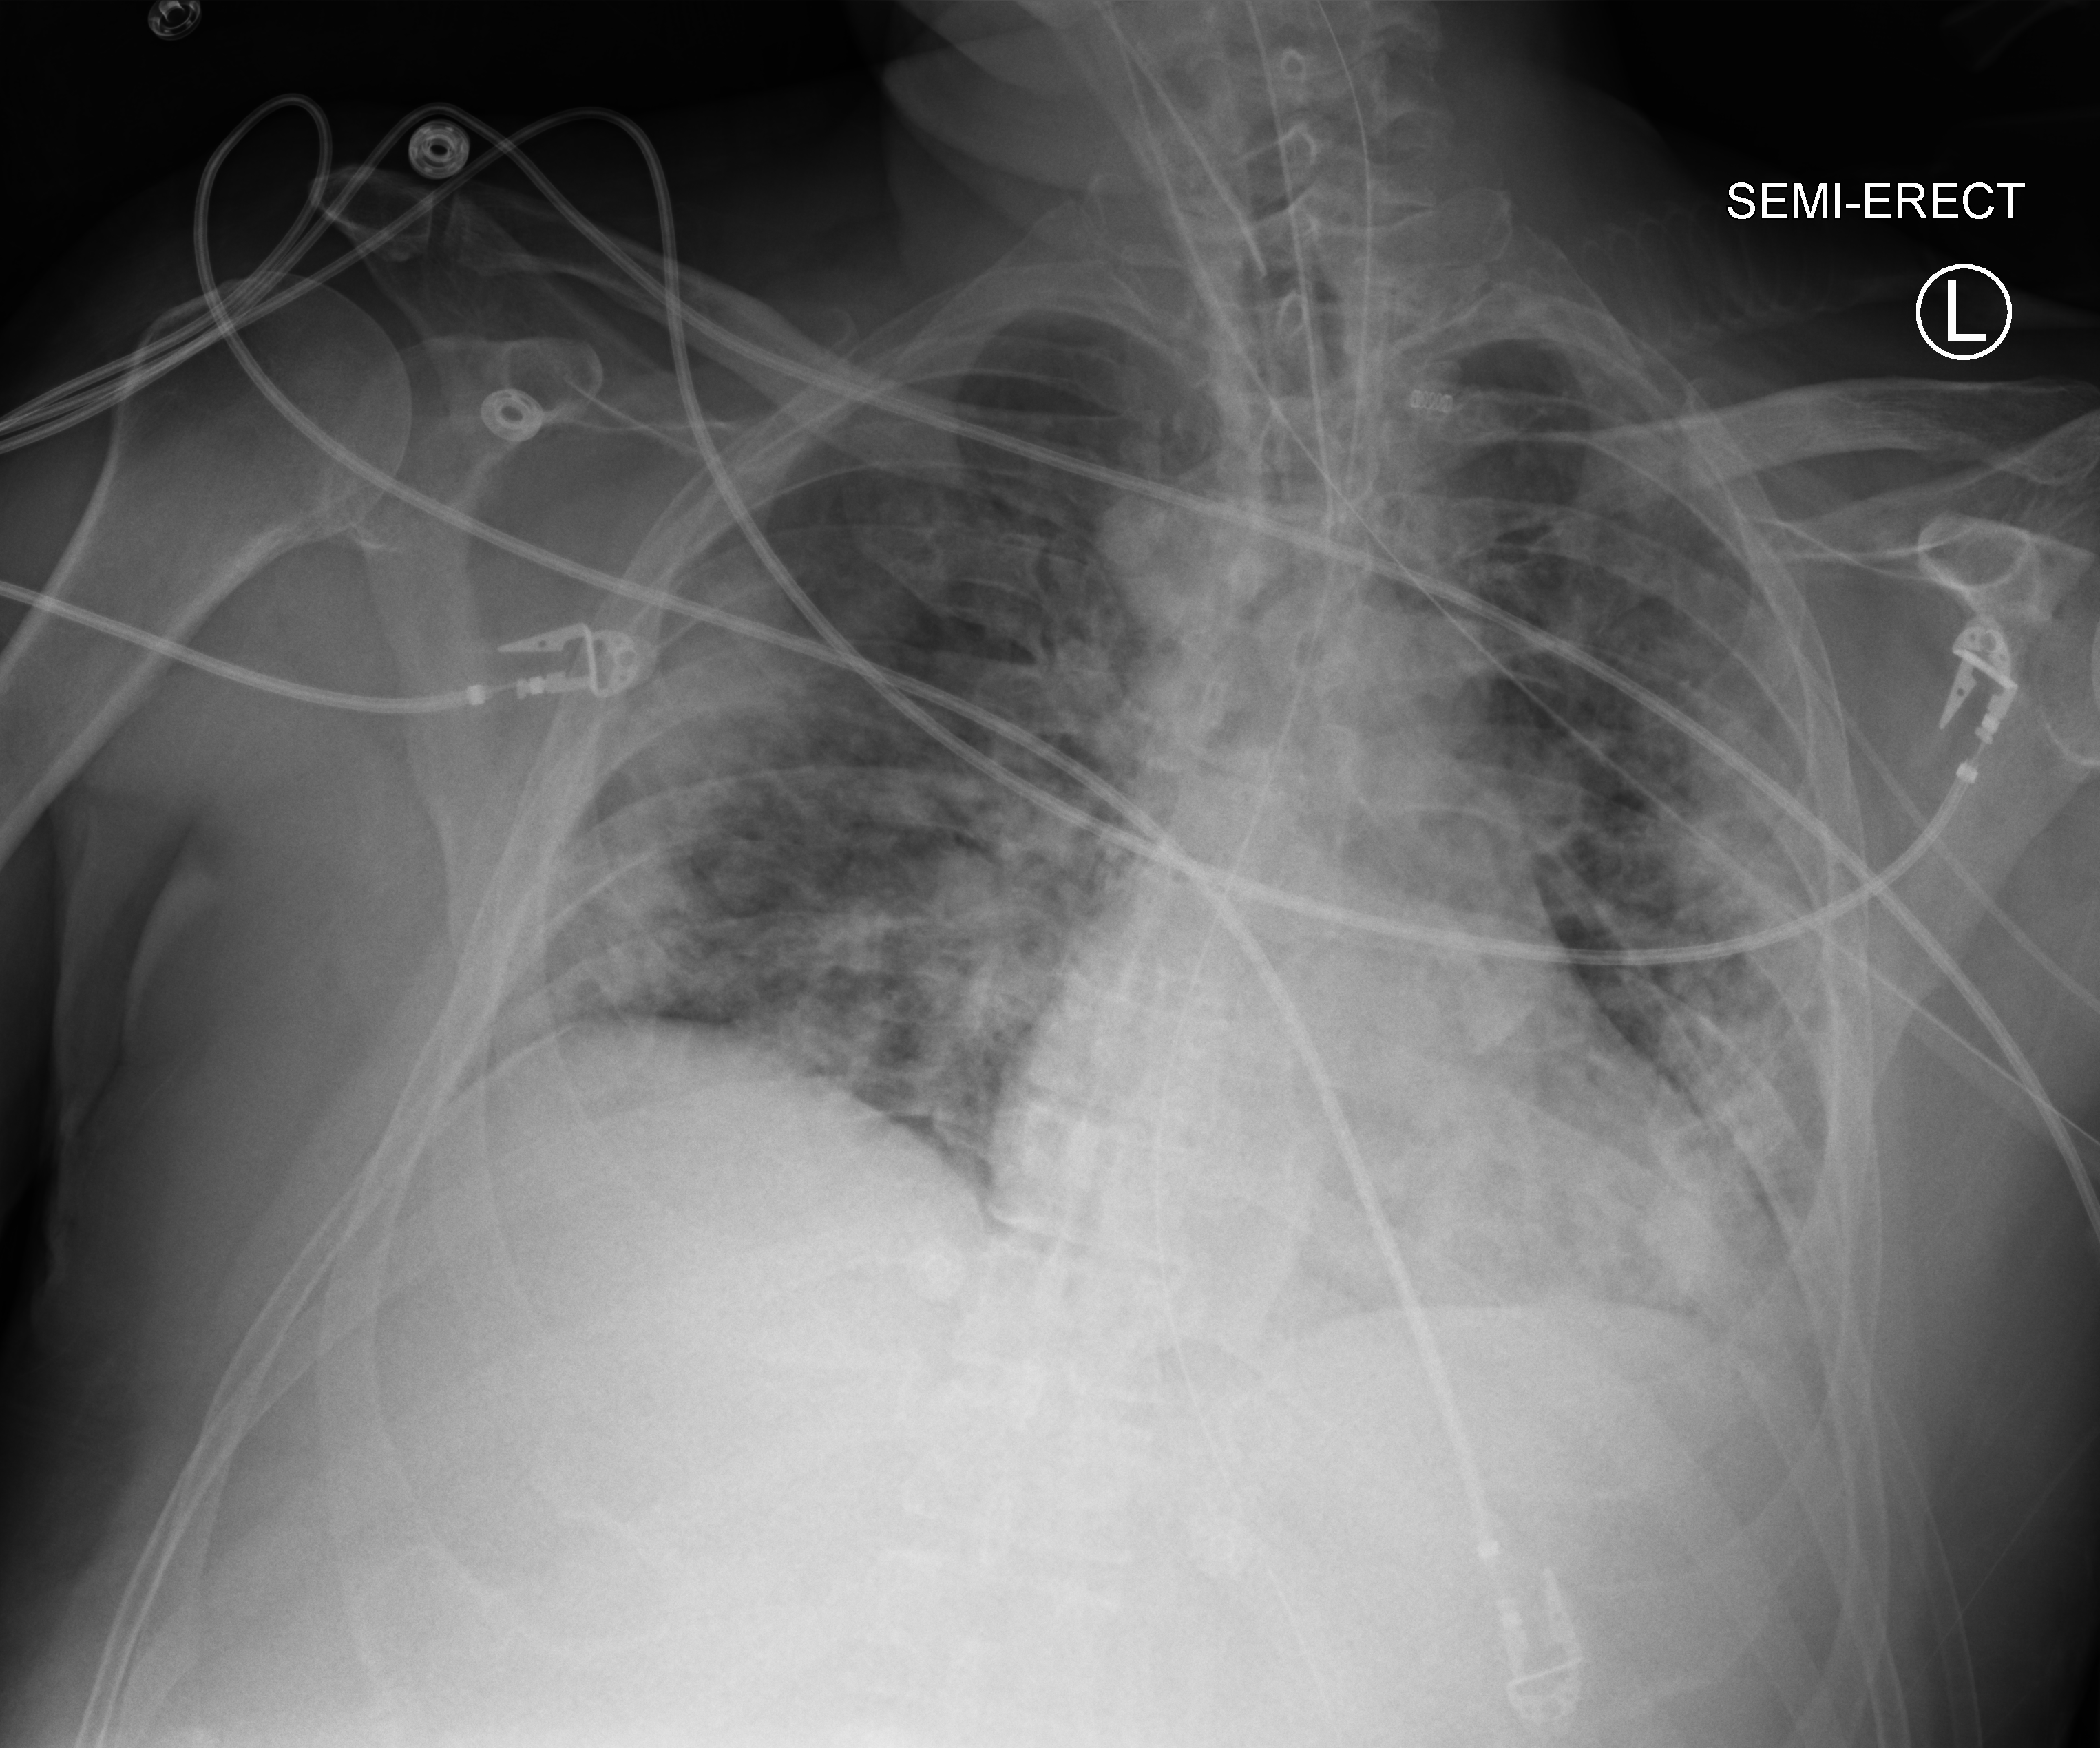
Bedside chest radiograph (computed radiography); anteroposterior (AP) projection. Patient hospitalised with COVID-19; male, aged 18–59 years.
From the hospital-stay record, not from the radiograph (when in the stay this image was taken is not recorded):
- smoking status (admission record): never